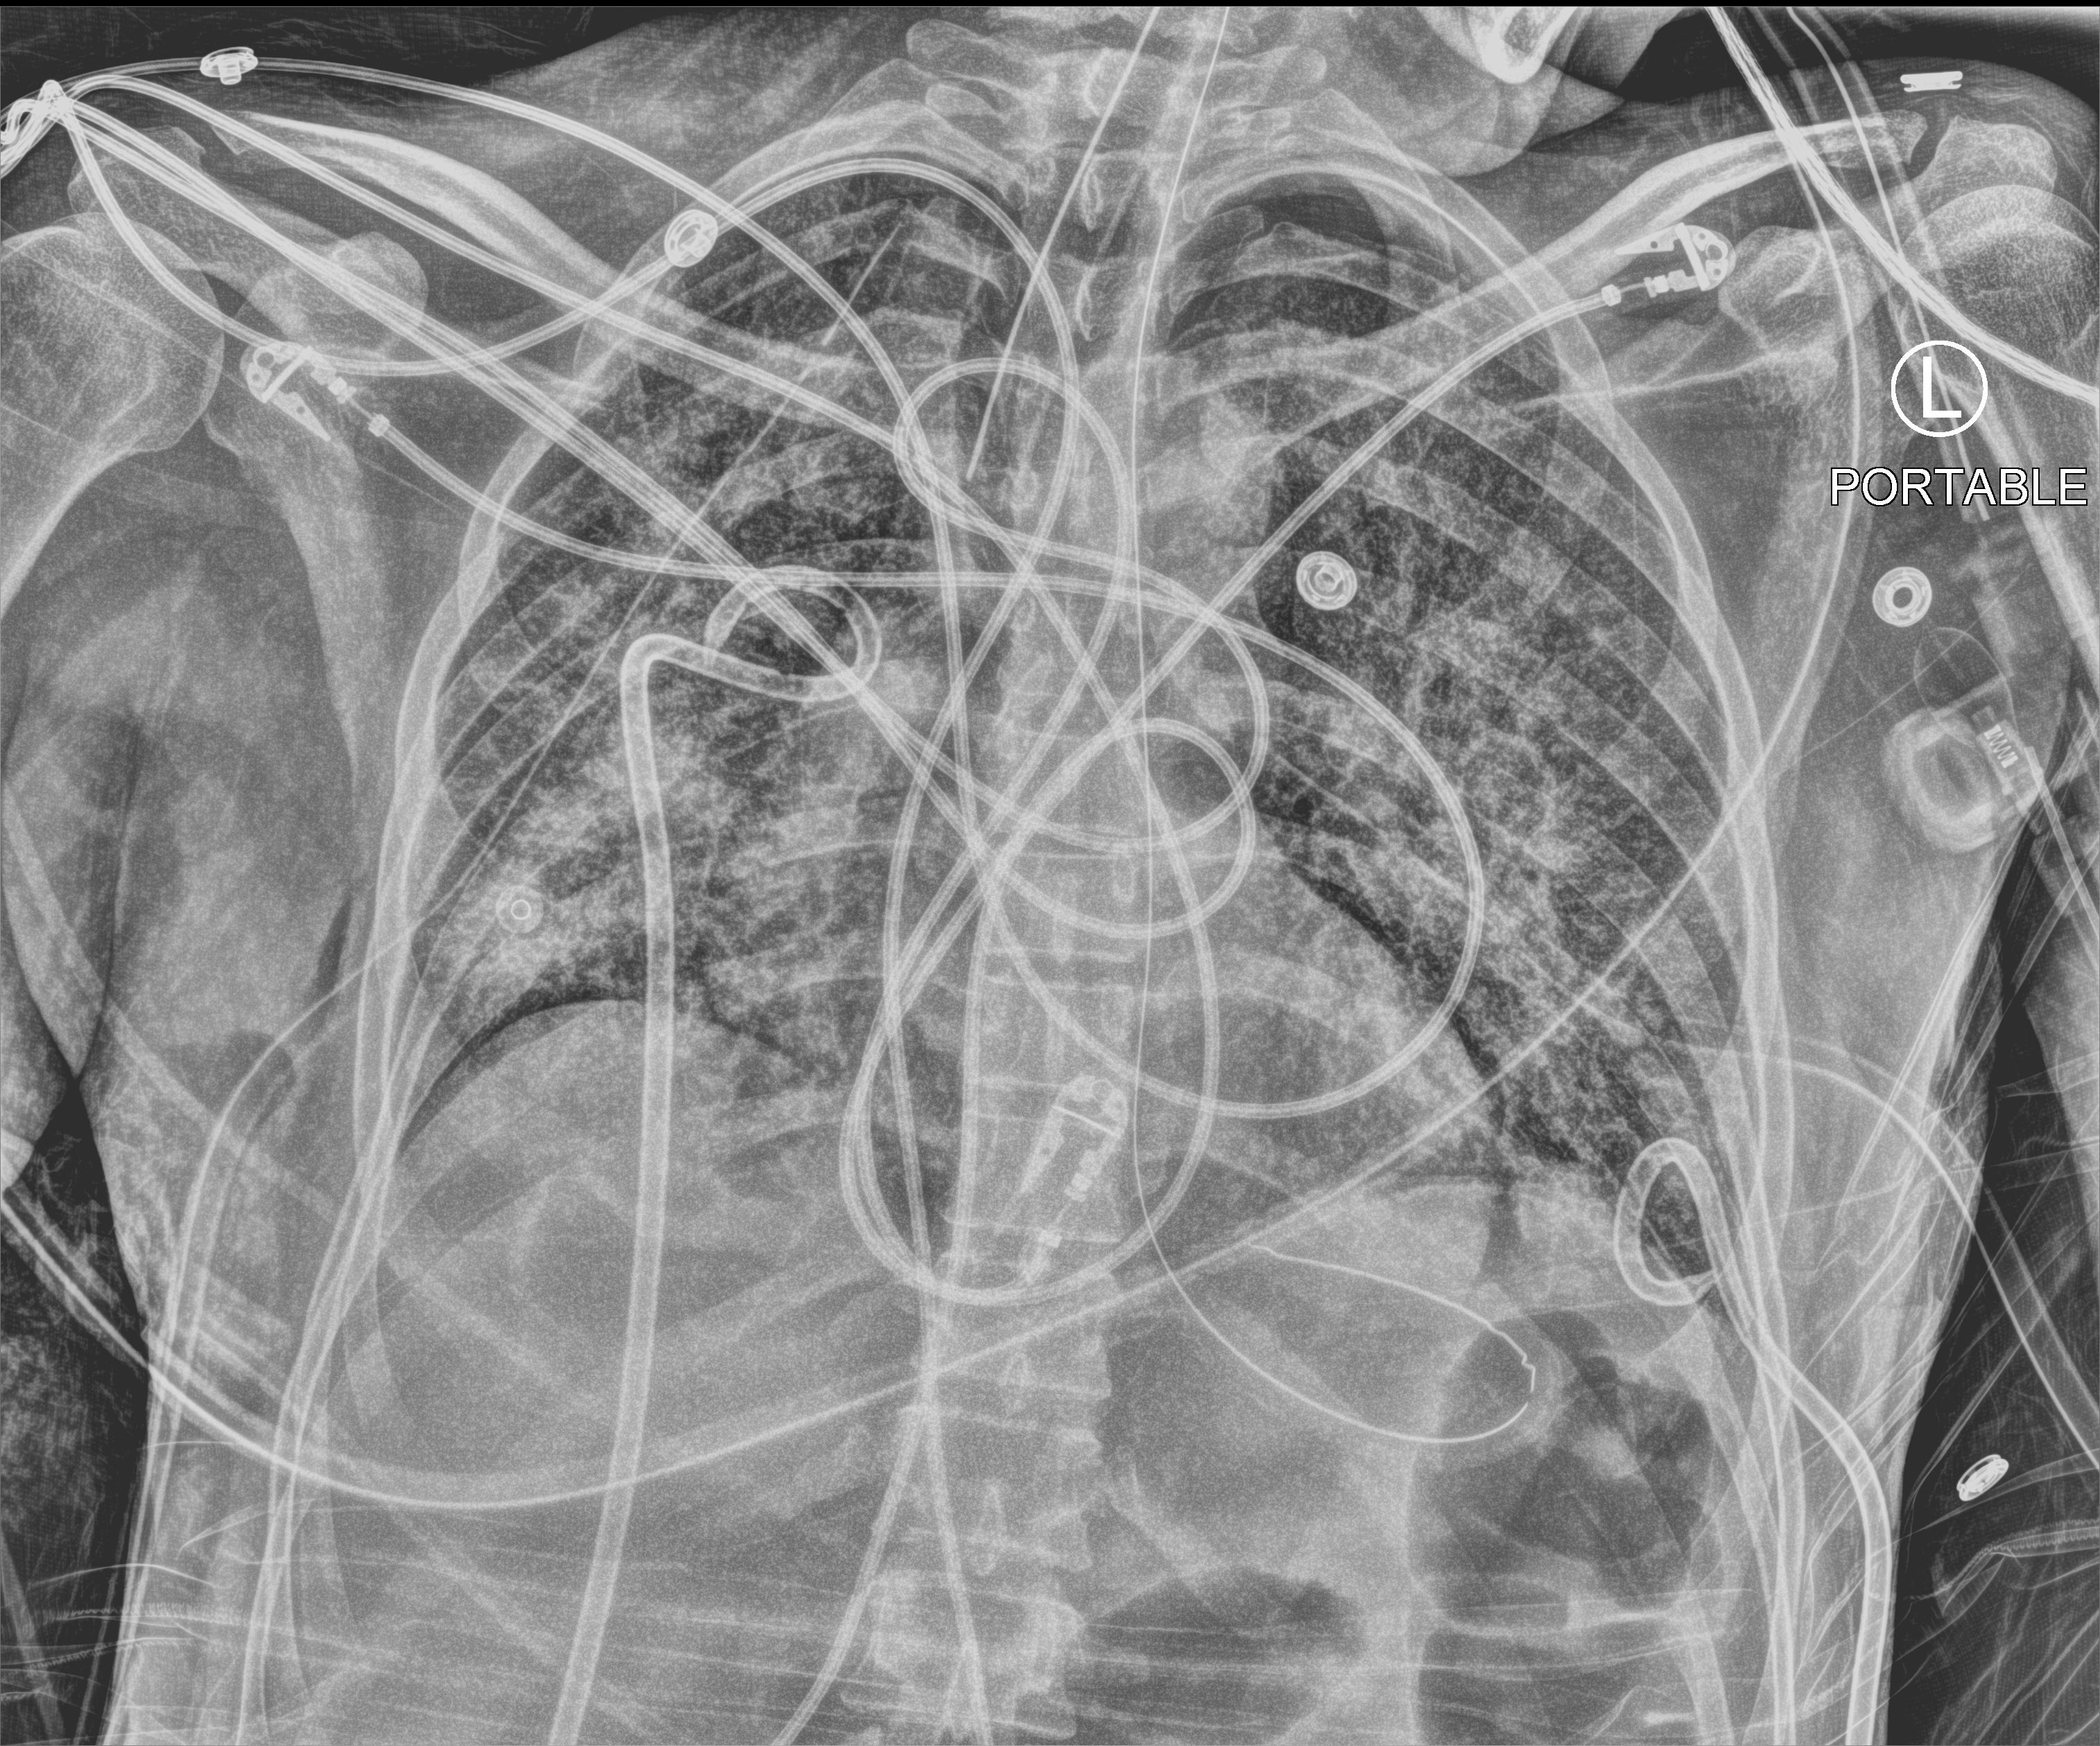
Portable chest radiograph, anteroposterior (AP) projection. Patient hospitalised with COVID-19, aged 18–59 years.
Admission-level facts for this patient (not findings on this image; timing relative to this image not recorded):
- admitted to intensive care during this hospital stay: yes
- length of hospital stay: 41 days